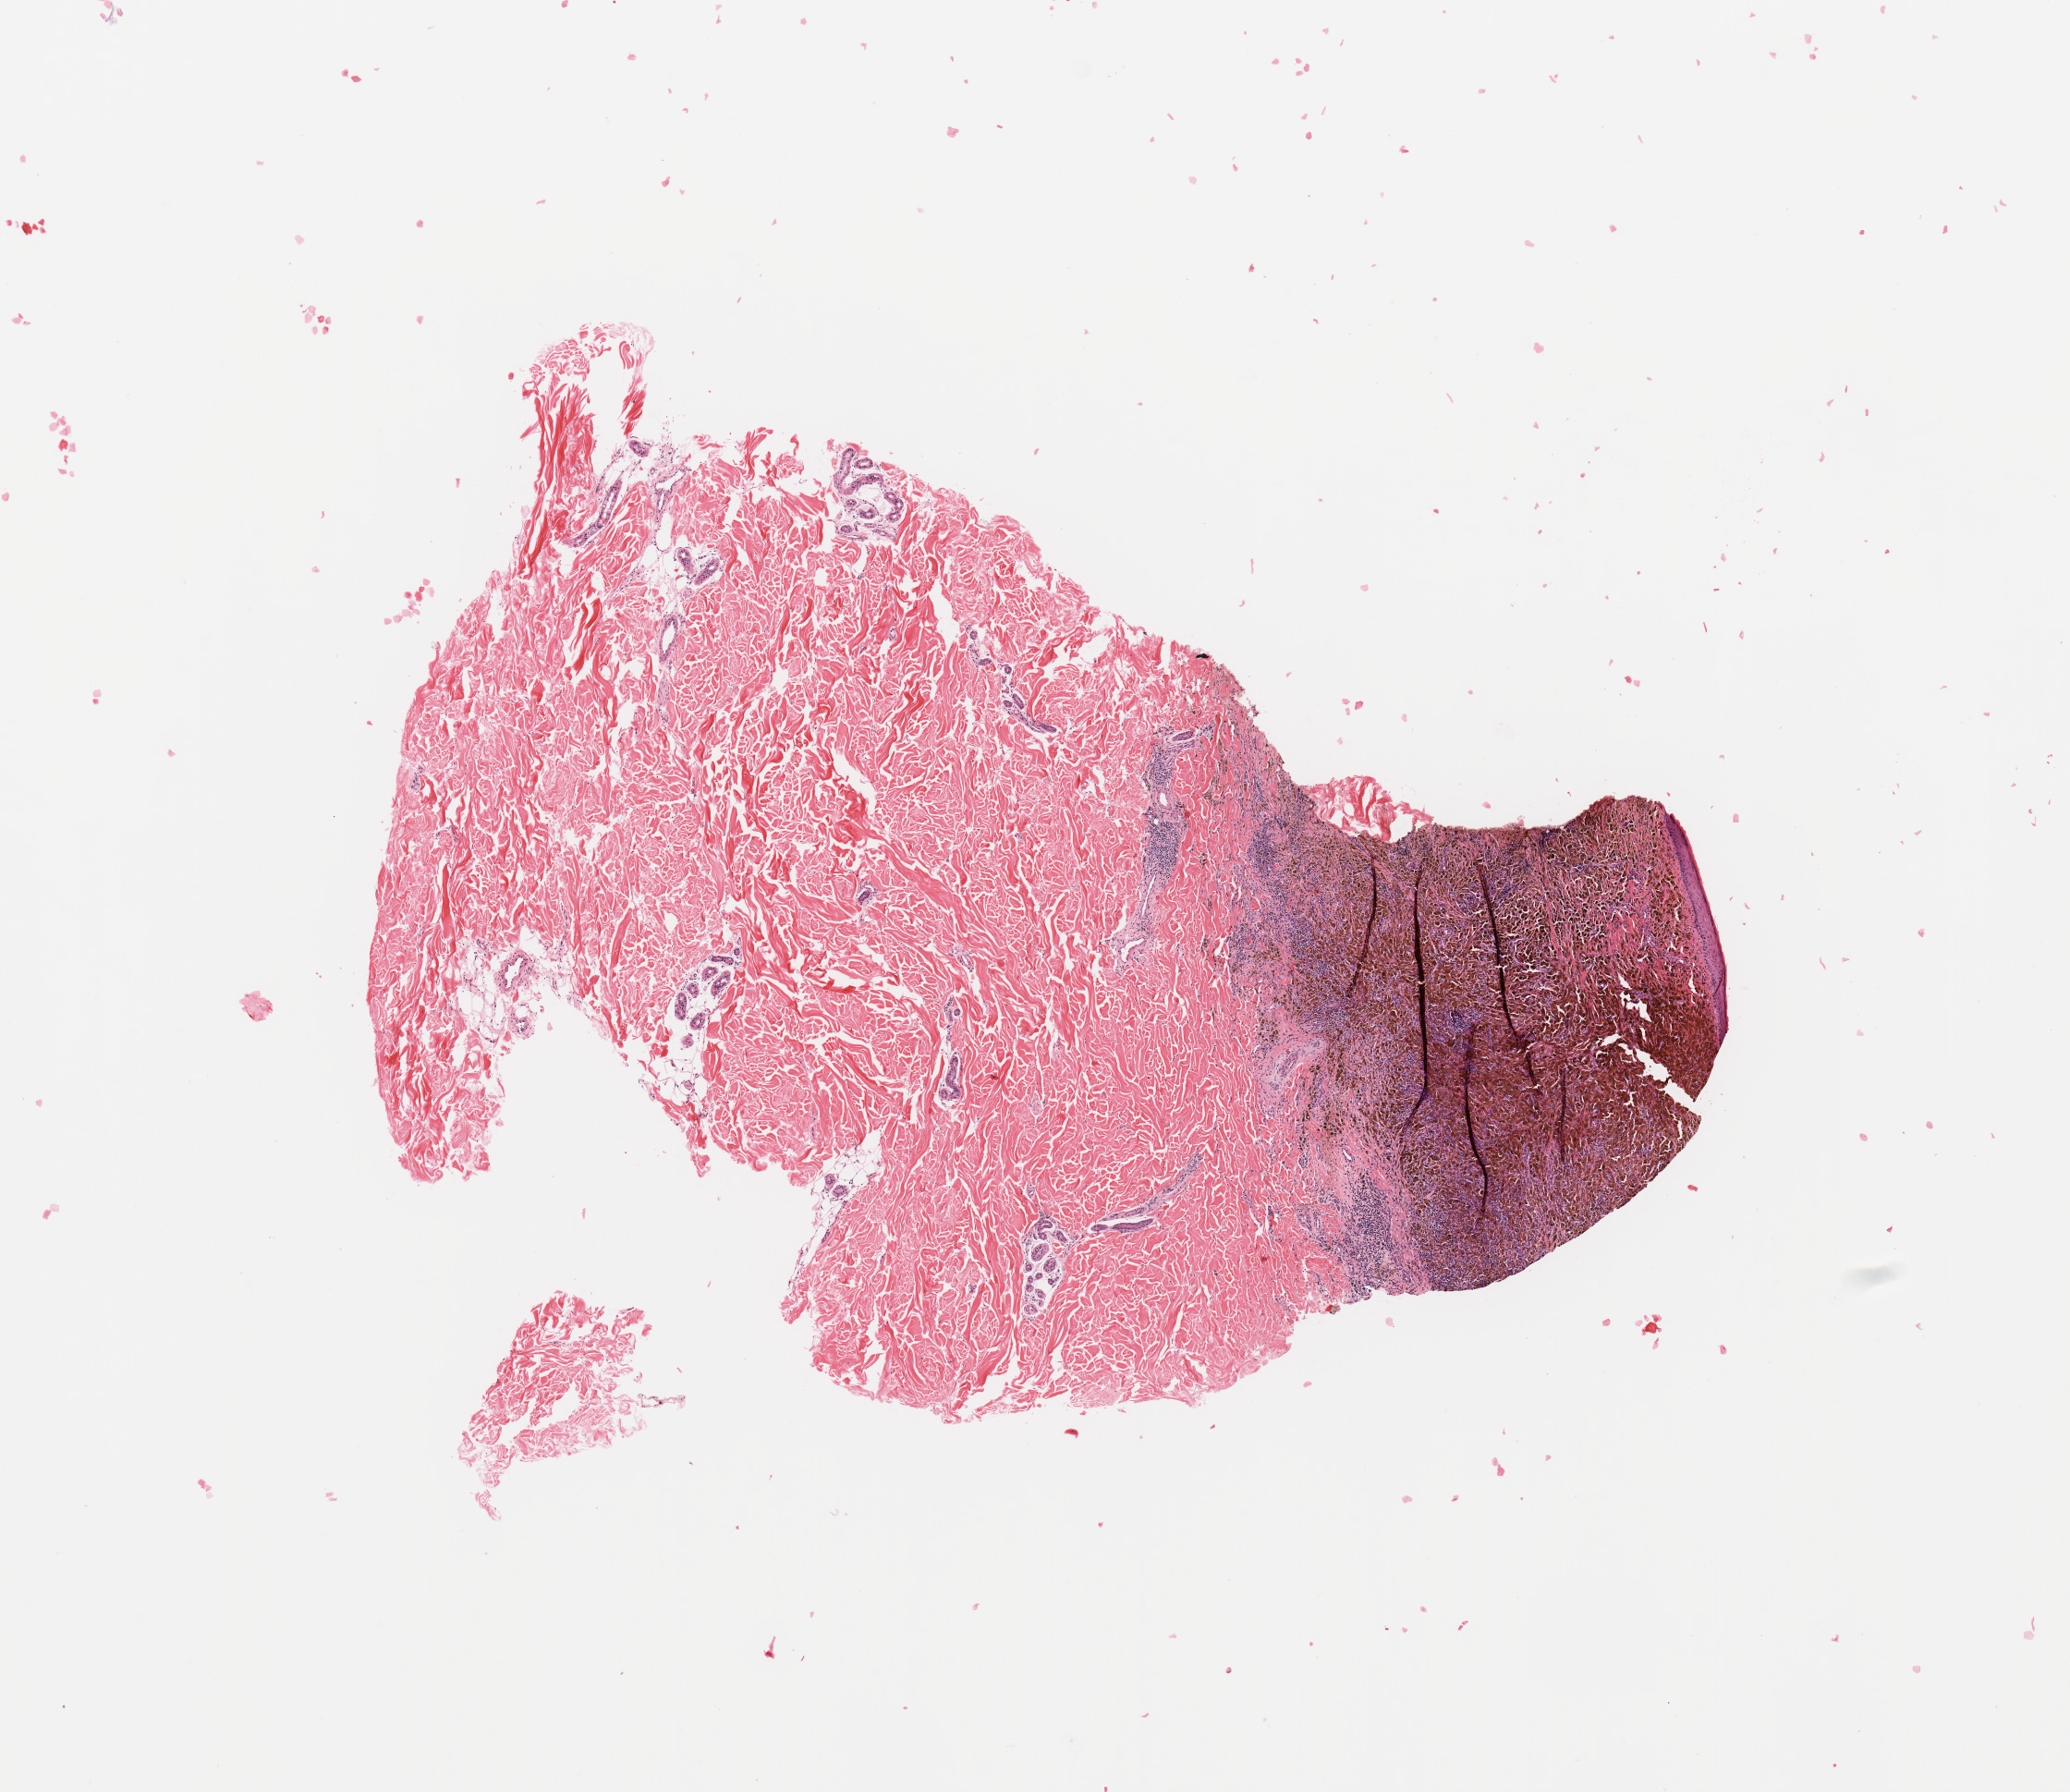
Hematoxylin and eosin (H&E) stained whole-slide image — shown as a low-resolution overview of the whole scanned area (about 8.9 x 7.7 mm, from a 20x scan), melanoma tumour tissue; sampled site not recorded. Female, 66 y/o.
Patient diagnosis (cohort enrolment): cutaneous melanoma (skin).